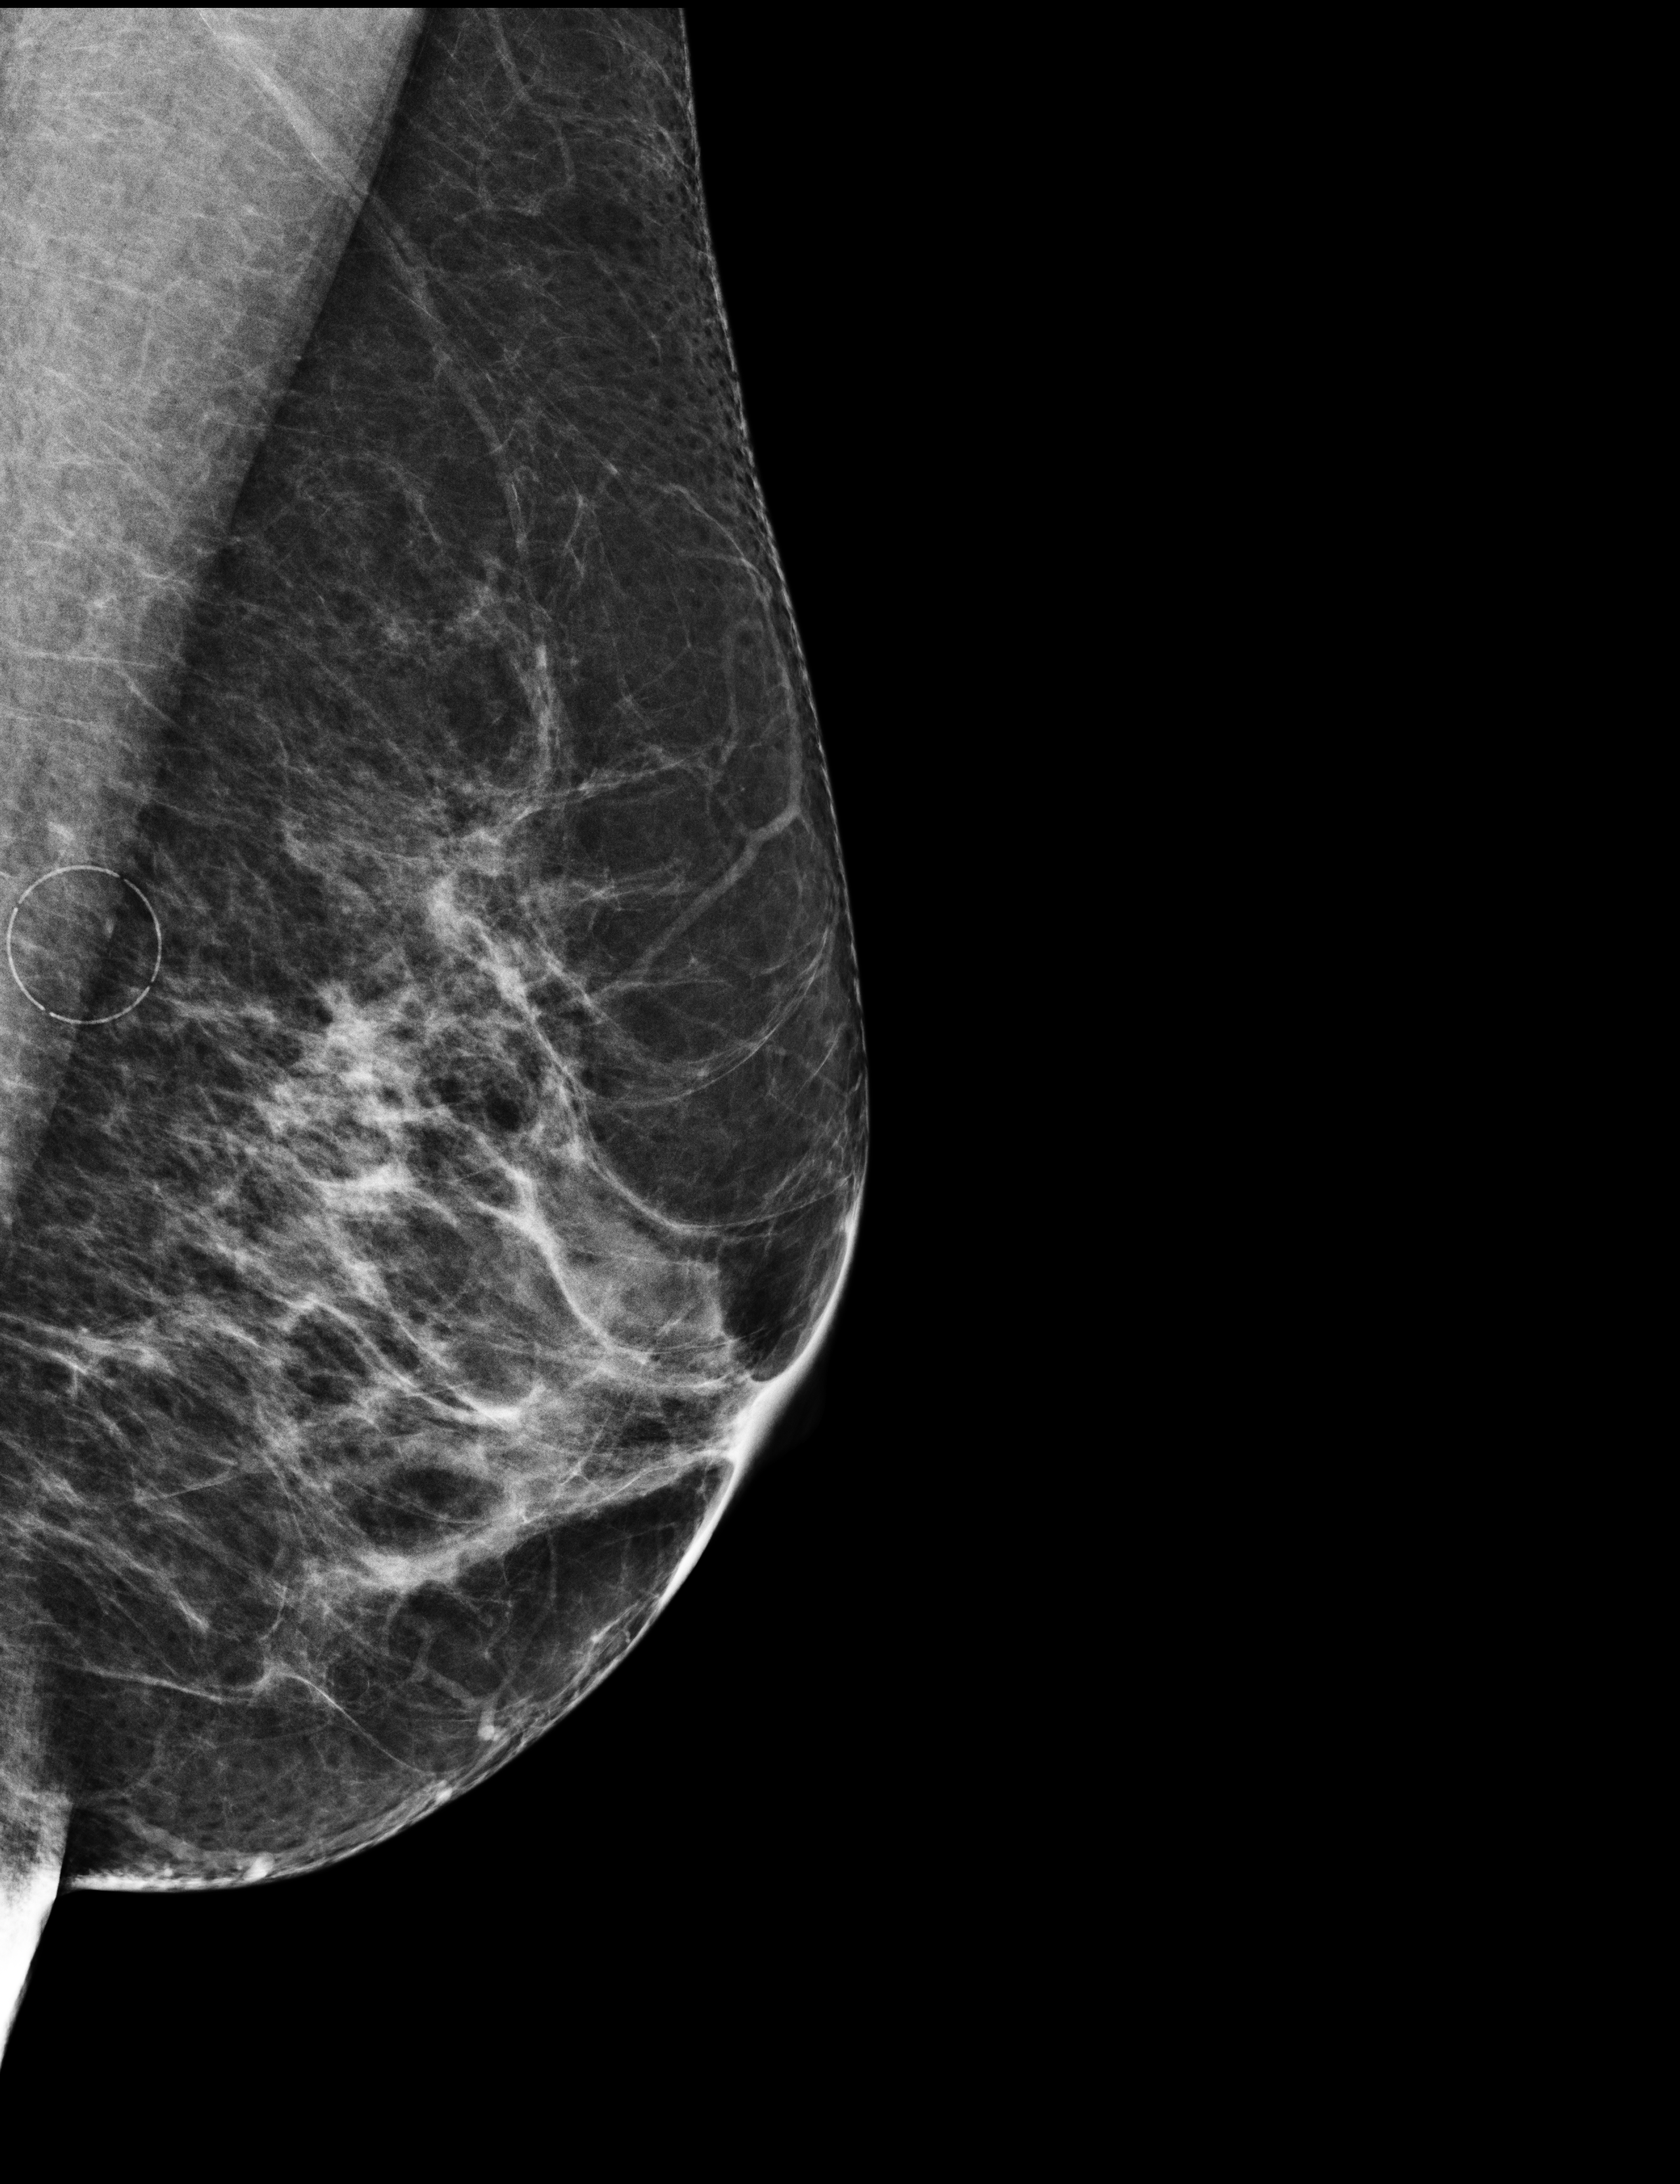
Annual screening mammography examination. Patient aged 61 years (female).
Image type: full-field digital mammogram. Breast: left. Projection: mediolateral (ML) view.